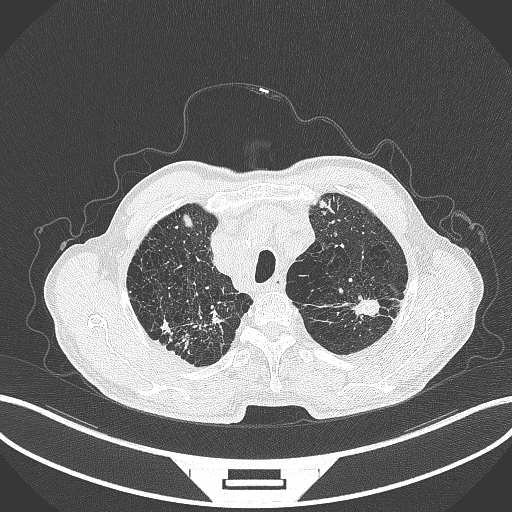
Chest CT, one axial slice. Slice 374 of 463 in the series (ordered by position). Reconstruction kernel B70f. 120 kVp. Lung window (W 1500 / L -600 HU). 1 mm slice thickness. 512 × 512 image matrix, field of view 400 × 400 mm. Patient: male, 74 years. Case-level facts recorded for this patient, not image findings: clinical TNM (as recorded): T2a N1 M0.
Outlined on this slice (bounding box drawn by a radiologist):
- lung tumour (recorded histology: adenocarcinoma): bounding box (x1, y1, x2, y2) in pixels: (348, 297, 390, 324)